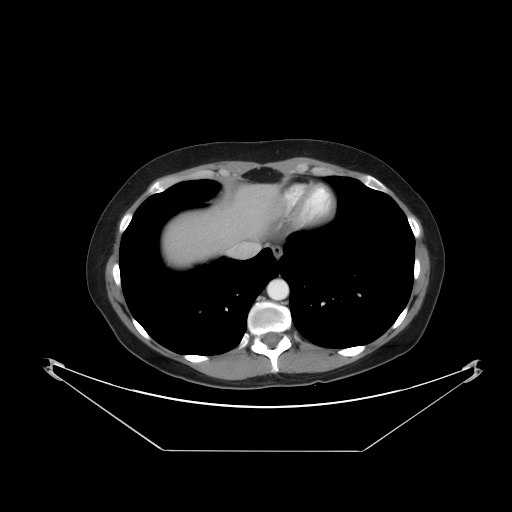
Contrast-enhanced abdominal CT, one axial slice. Position 43 of 48 along the scan axis. Reconstruction kernel STANDARD. 120 kVp. Intravenous contrast given. Soft-tissue window (W 400 / L 40 HU). 5 mm slice thickness. 512 × 512 image matrix. Female patient, age 38 years. From the clinical record (not read from this slice): diagnosis: colorectal cancer liver metastases, imaged before liver resection; multiple liver metastases: yes; largest metastasis: 2.5 cm; chemotherapy before resection: no.
Annotated regions visible in this slice (manually delineated by an expert):
- liver: box from (x=163, y=186) to (x=284, y=267) px
- planned liver remnant (the part of the liver to remain after resection): (x=224, y=186)–(x=284, y=241)